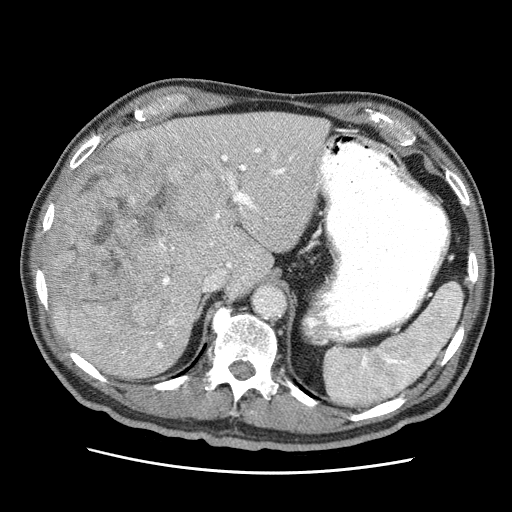
Contrast-enhanced abdominal CT (liver protocol), one axial slice. Position 39 of 75 along the scan axis. 120 kVp. Soft-tissue window (W 400 / L 40 HU). 512 × 512 image matrix, field of view 360 × 360 mm. Case-level facts recorded for this patient, not image findings: diagnosis: hepatocellular carcinoma (patient treated with transarterial chemoembolisation; whether this scan precedes or follows treatment is not stated here); TNM stage (as recorded): Stage-IIIA; Child-Pugh class: A; tumour size: 13.9 cm.
Structures marked on this image (semi-automatically segmented with operator editing):
- liver parenchyma outside the tumour (the mass and vessels are separate outlines, so this box may not span the whole liver): bounding box (x1, y1, x2, y2) in pixels: (46, 112, 330, 378)
- mass: (49, 138, 227, 338)
- liver vessels: (59, 117, 297, 367)